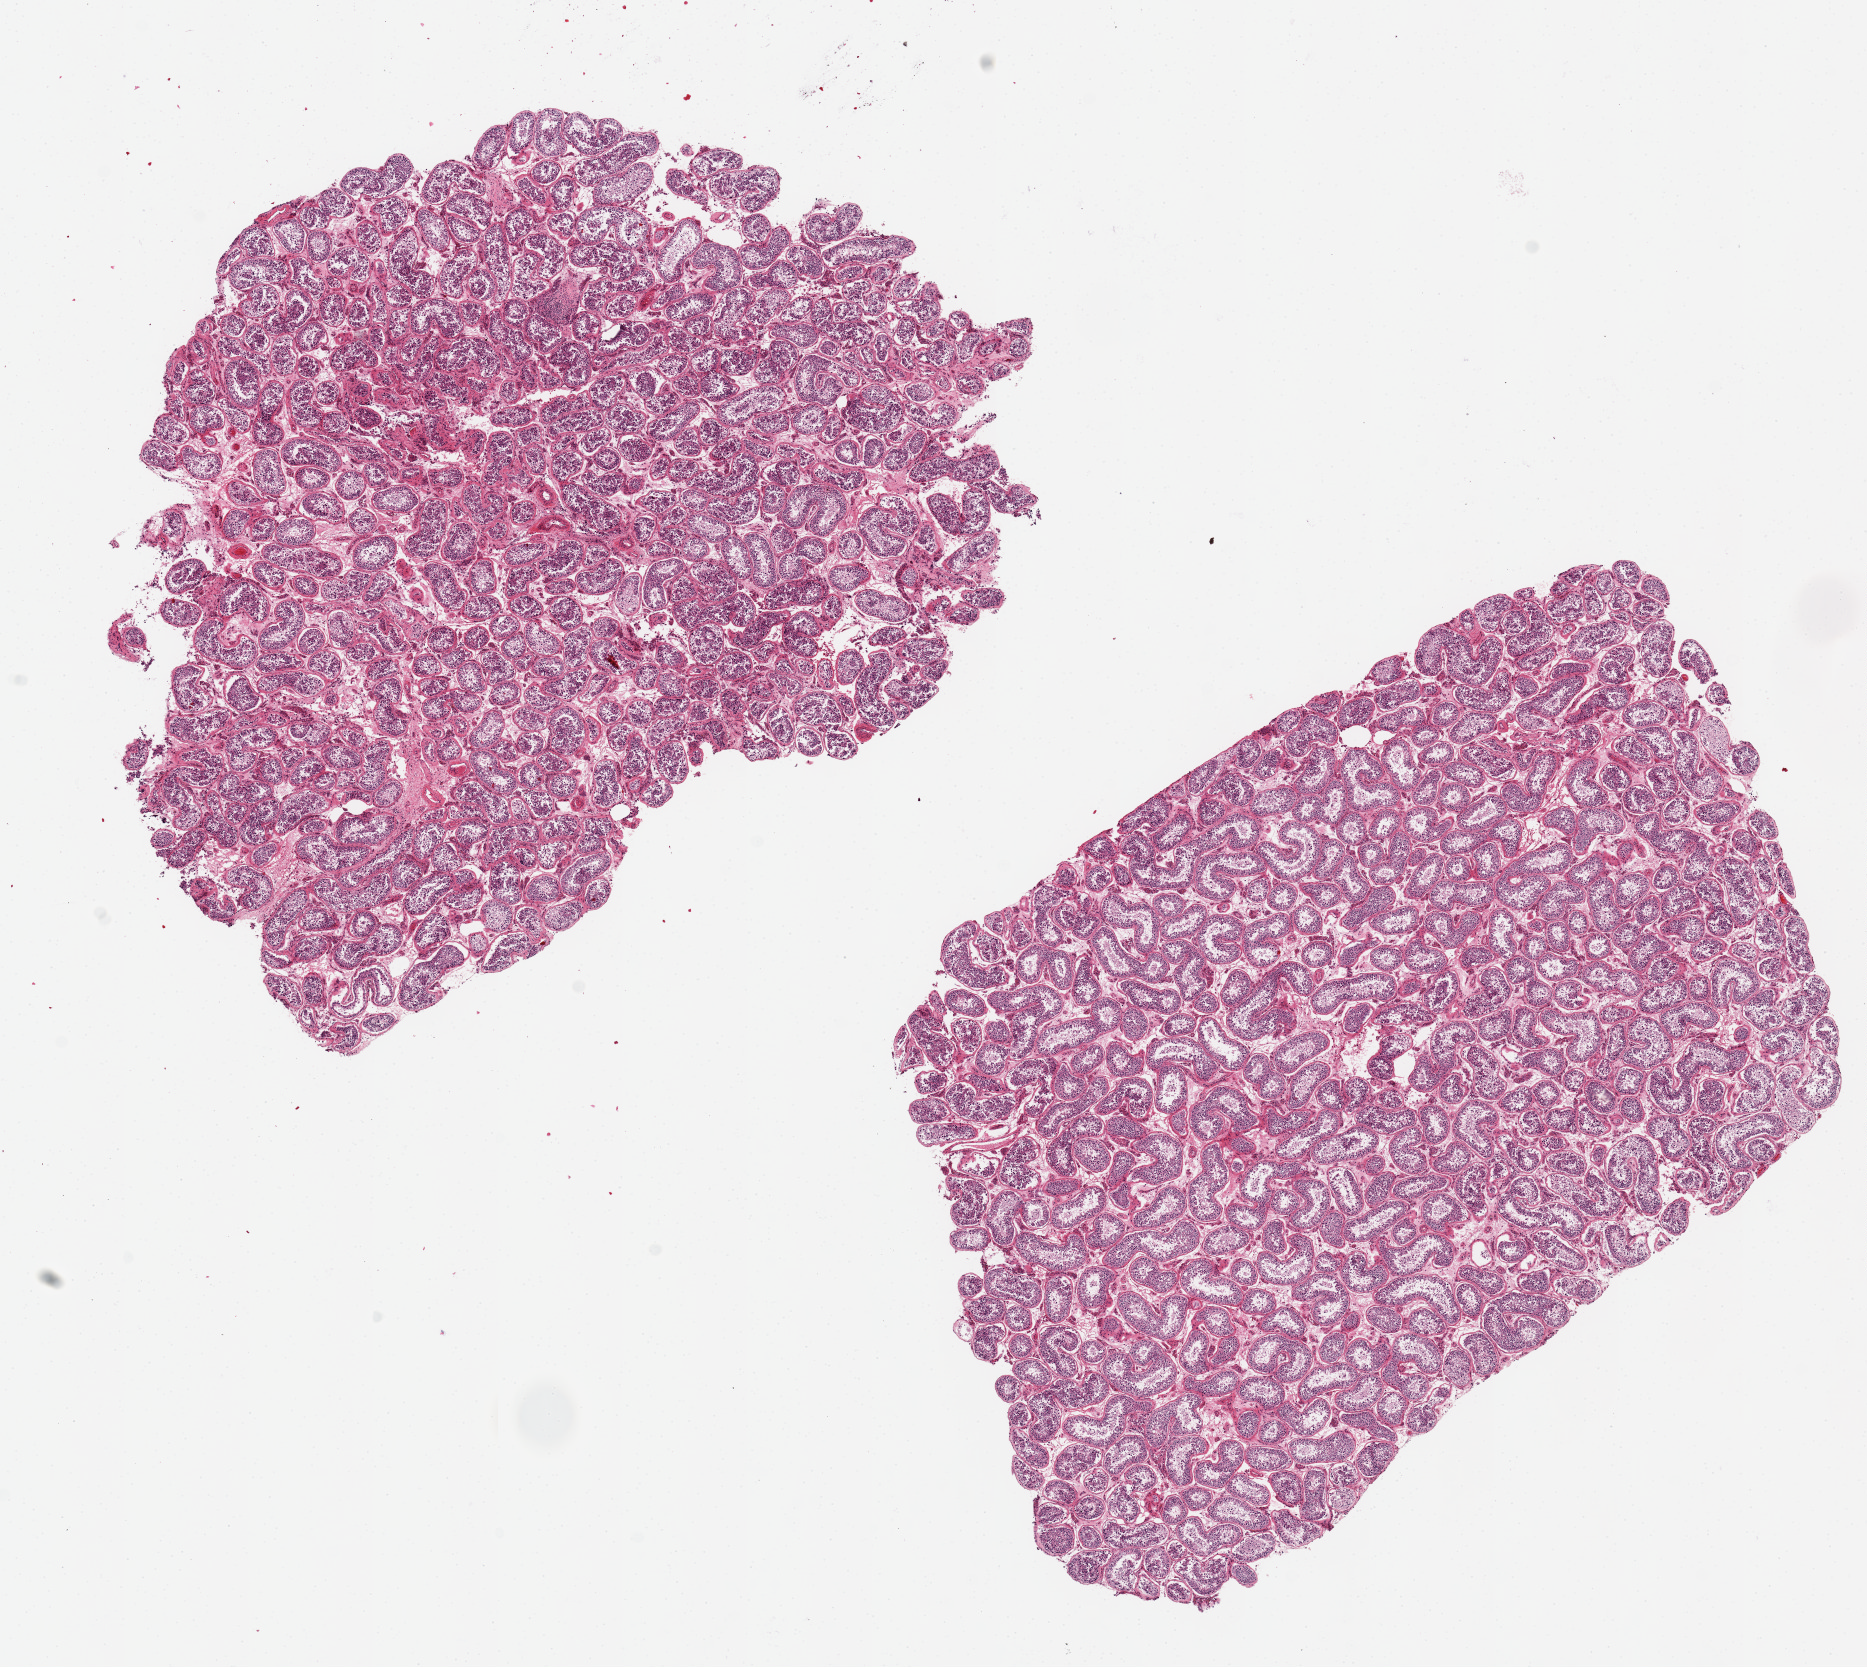
Digitized hematoxylin and eosin (H&E)-stained section, whole scanned area (about 14.8 x 13.2 mm) shown as a low-resolution overview; PAXgene-fixed, paraffin-embedded tissue; target tissue: testis; tissue donor sample.
• review note (as recorded): 2 ~7.5x5.5mm aliquots. Mature spermatozoa are evident